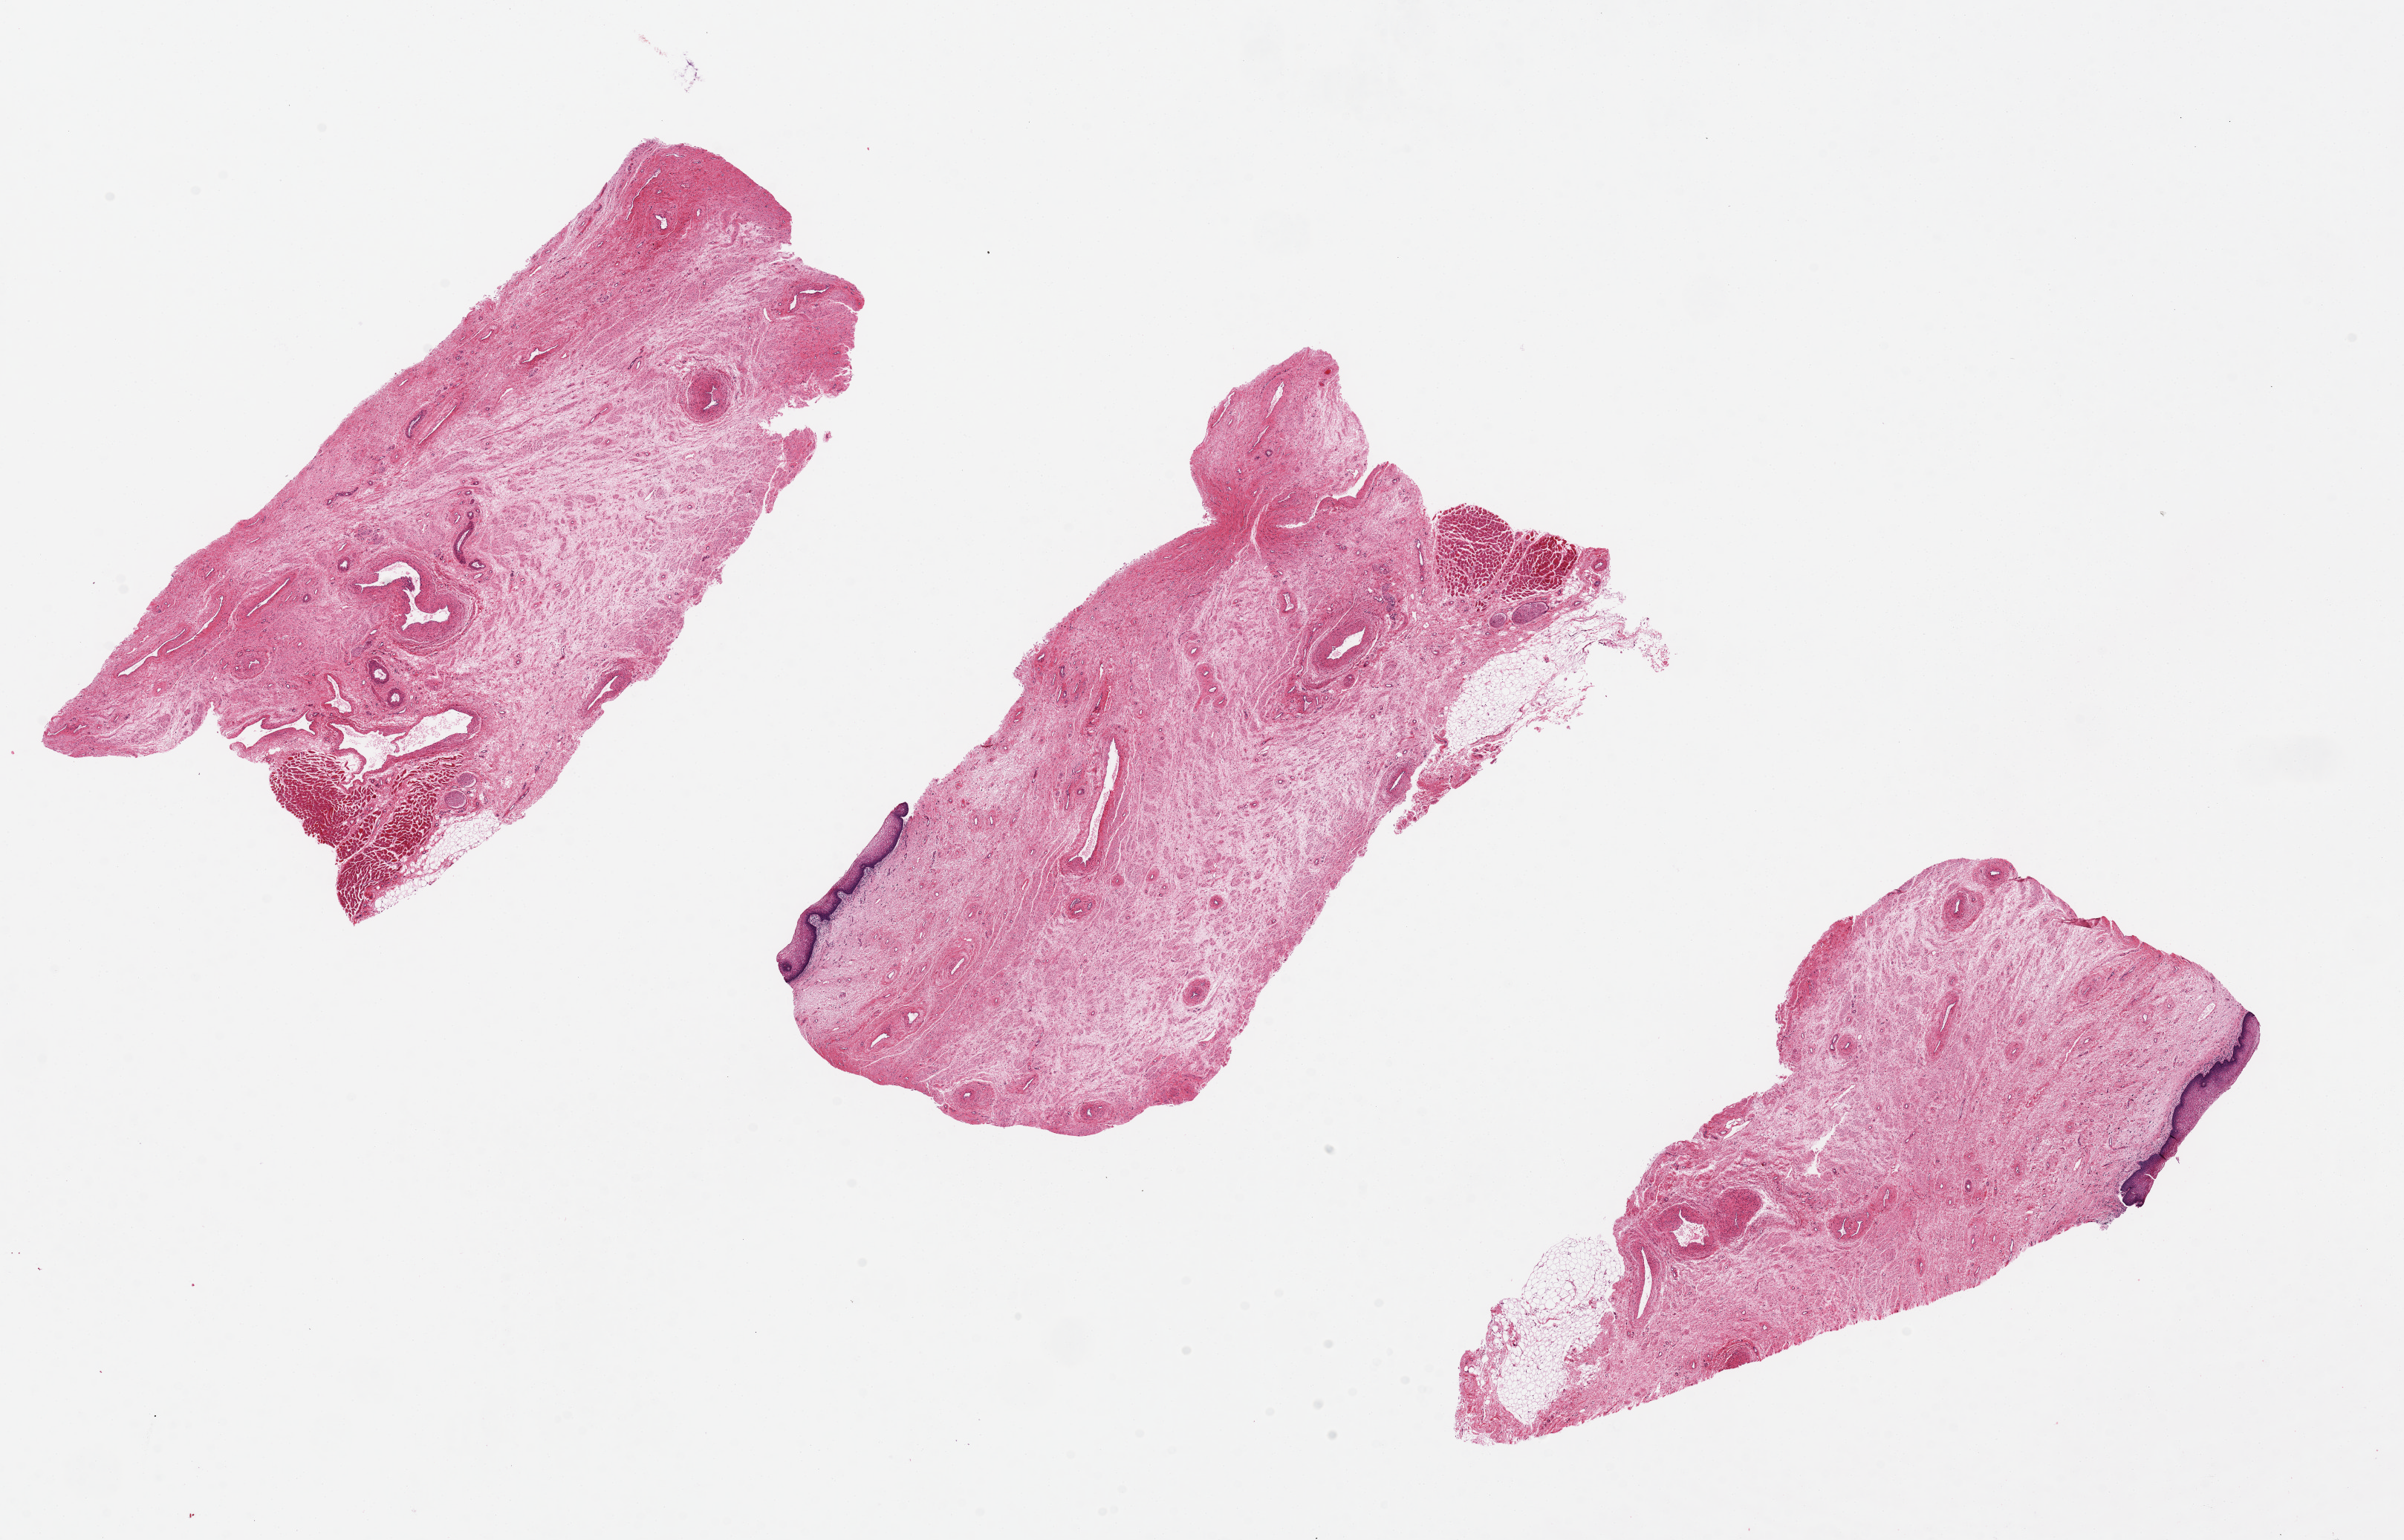
Whole-slide image, H&E stain, whole scanned area (about 25.6 x 16.4 mm) shown as a low-resolution overview, PAXgene-fixed paraffin-embedded (PFPE) section, section of vagina (target tissue), donor tissue sample. Donor sex: female.
Reviewer comment on this tissue sample: Minimal epithelium.